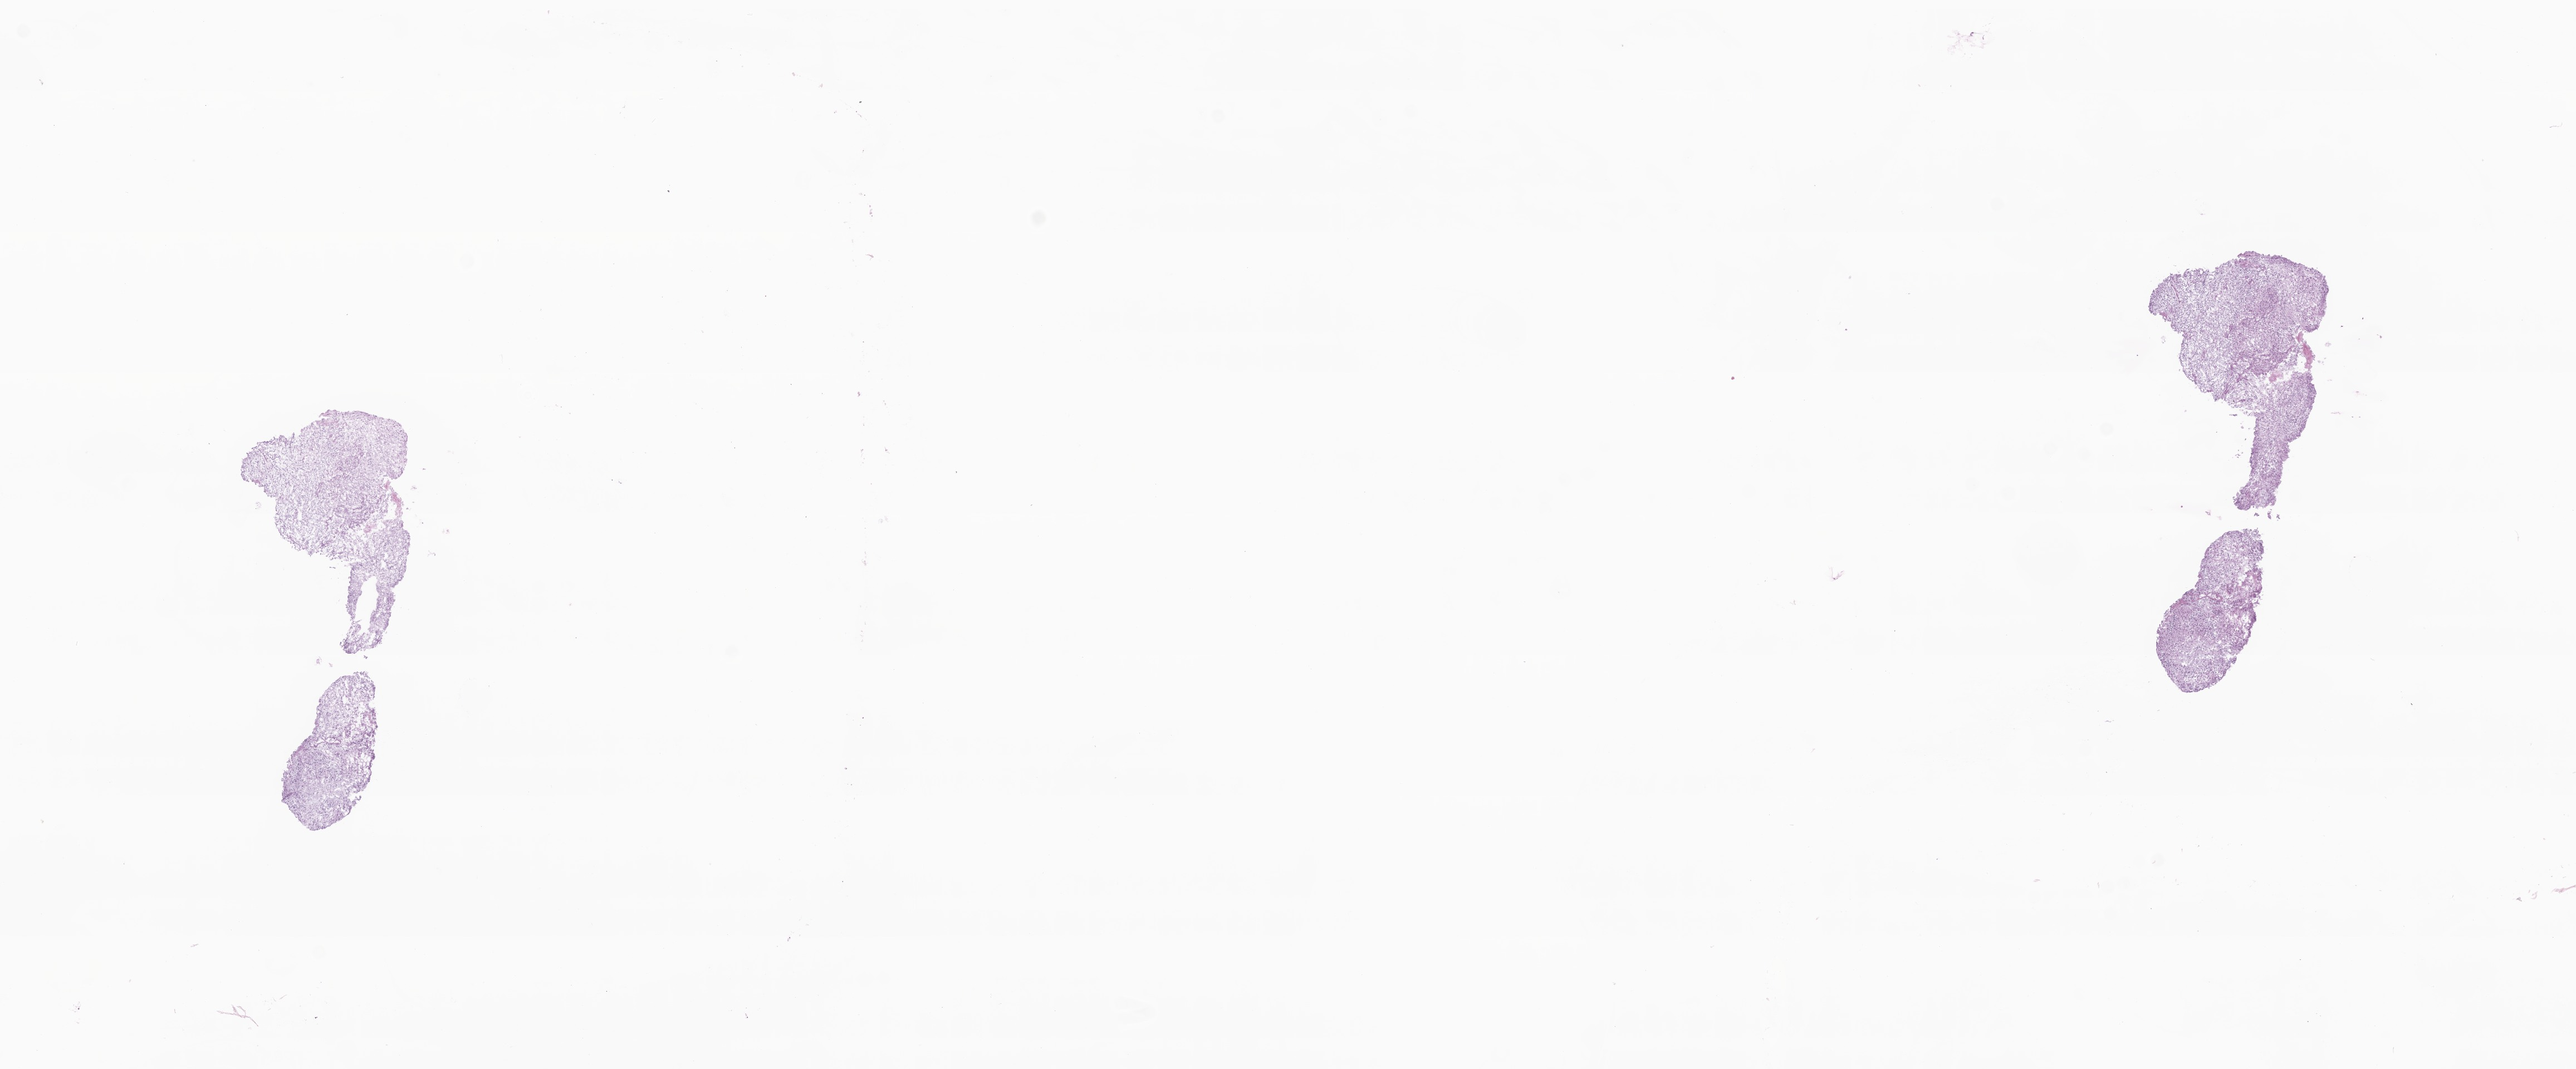
Whole-slide image, H&E stain — low-resolution overview of the scanned area, about 19.5 x 8.1 mm, frozen section, specimen: primary tumor, anatomic site: brain. Female patient; age at initial diagnosis 78 years.
Histologic diagnosis: Glioblastoma, NOS.